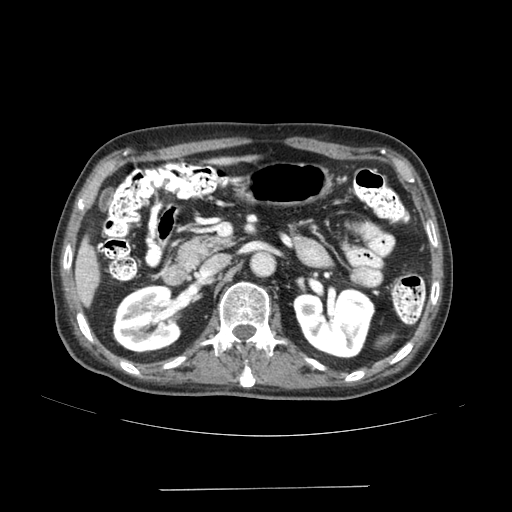
Contrast-enhanced abdominal CT (liver protocol), one axial slice. Position 64 of 192 along the scan axis. Reconstruction kernel SOFT. 120 kVp. Soft-tissue window (W 400 / L 40 HU). 2.5 mm slice thickness. 512 × 512 image matrix, field of view 400 × 400 mm. From the clinical record (not read from this slice): diagnosis: hepatocellular carcinoma (patient treated with transarterial chemoembolisation; whether this scan precedes or follows treatment is not stated here); TNM stage (as recorded): Stage-IVA; Child-Pugh class: A; tumour nodularity: uninodular.
Annotated regions visible in this slice (semi-automatically segmented with operator editing):
- liver parenchyma outside the tumour (the mass and vessels are separate outlines, so this box may not span the whole liver): bounding box [x1, y1, x2, y2] px = [74, 238, 100, 306]